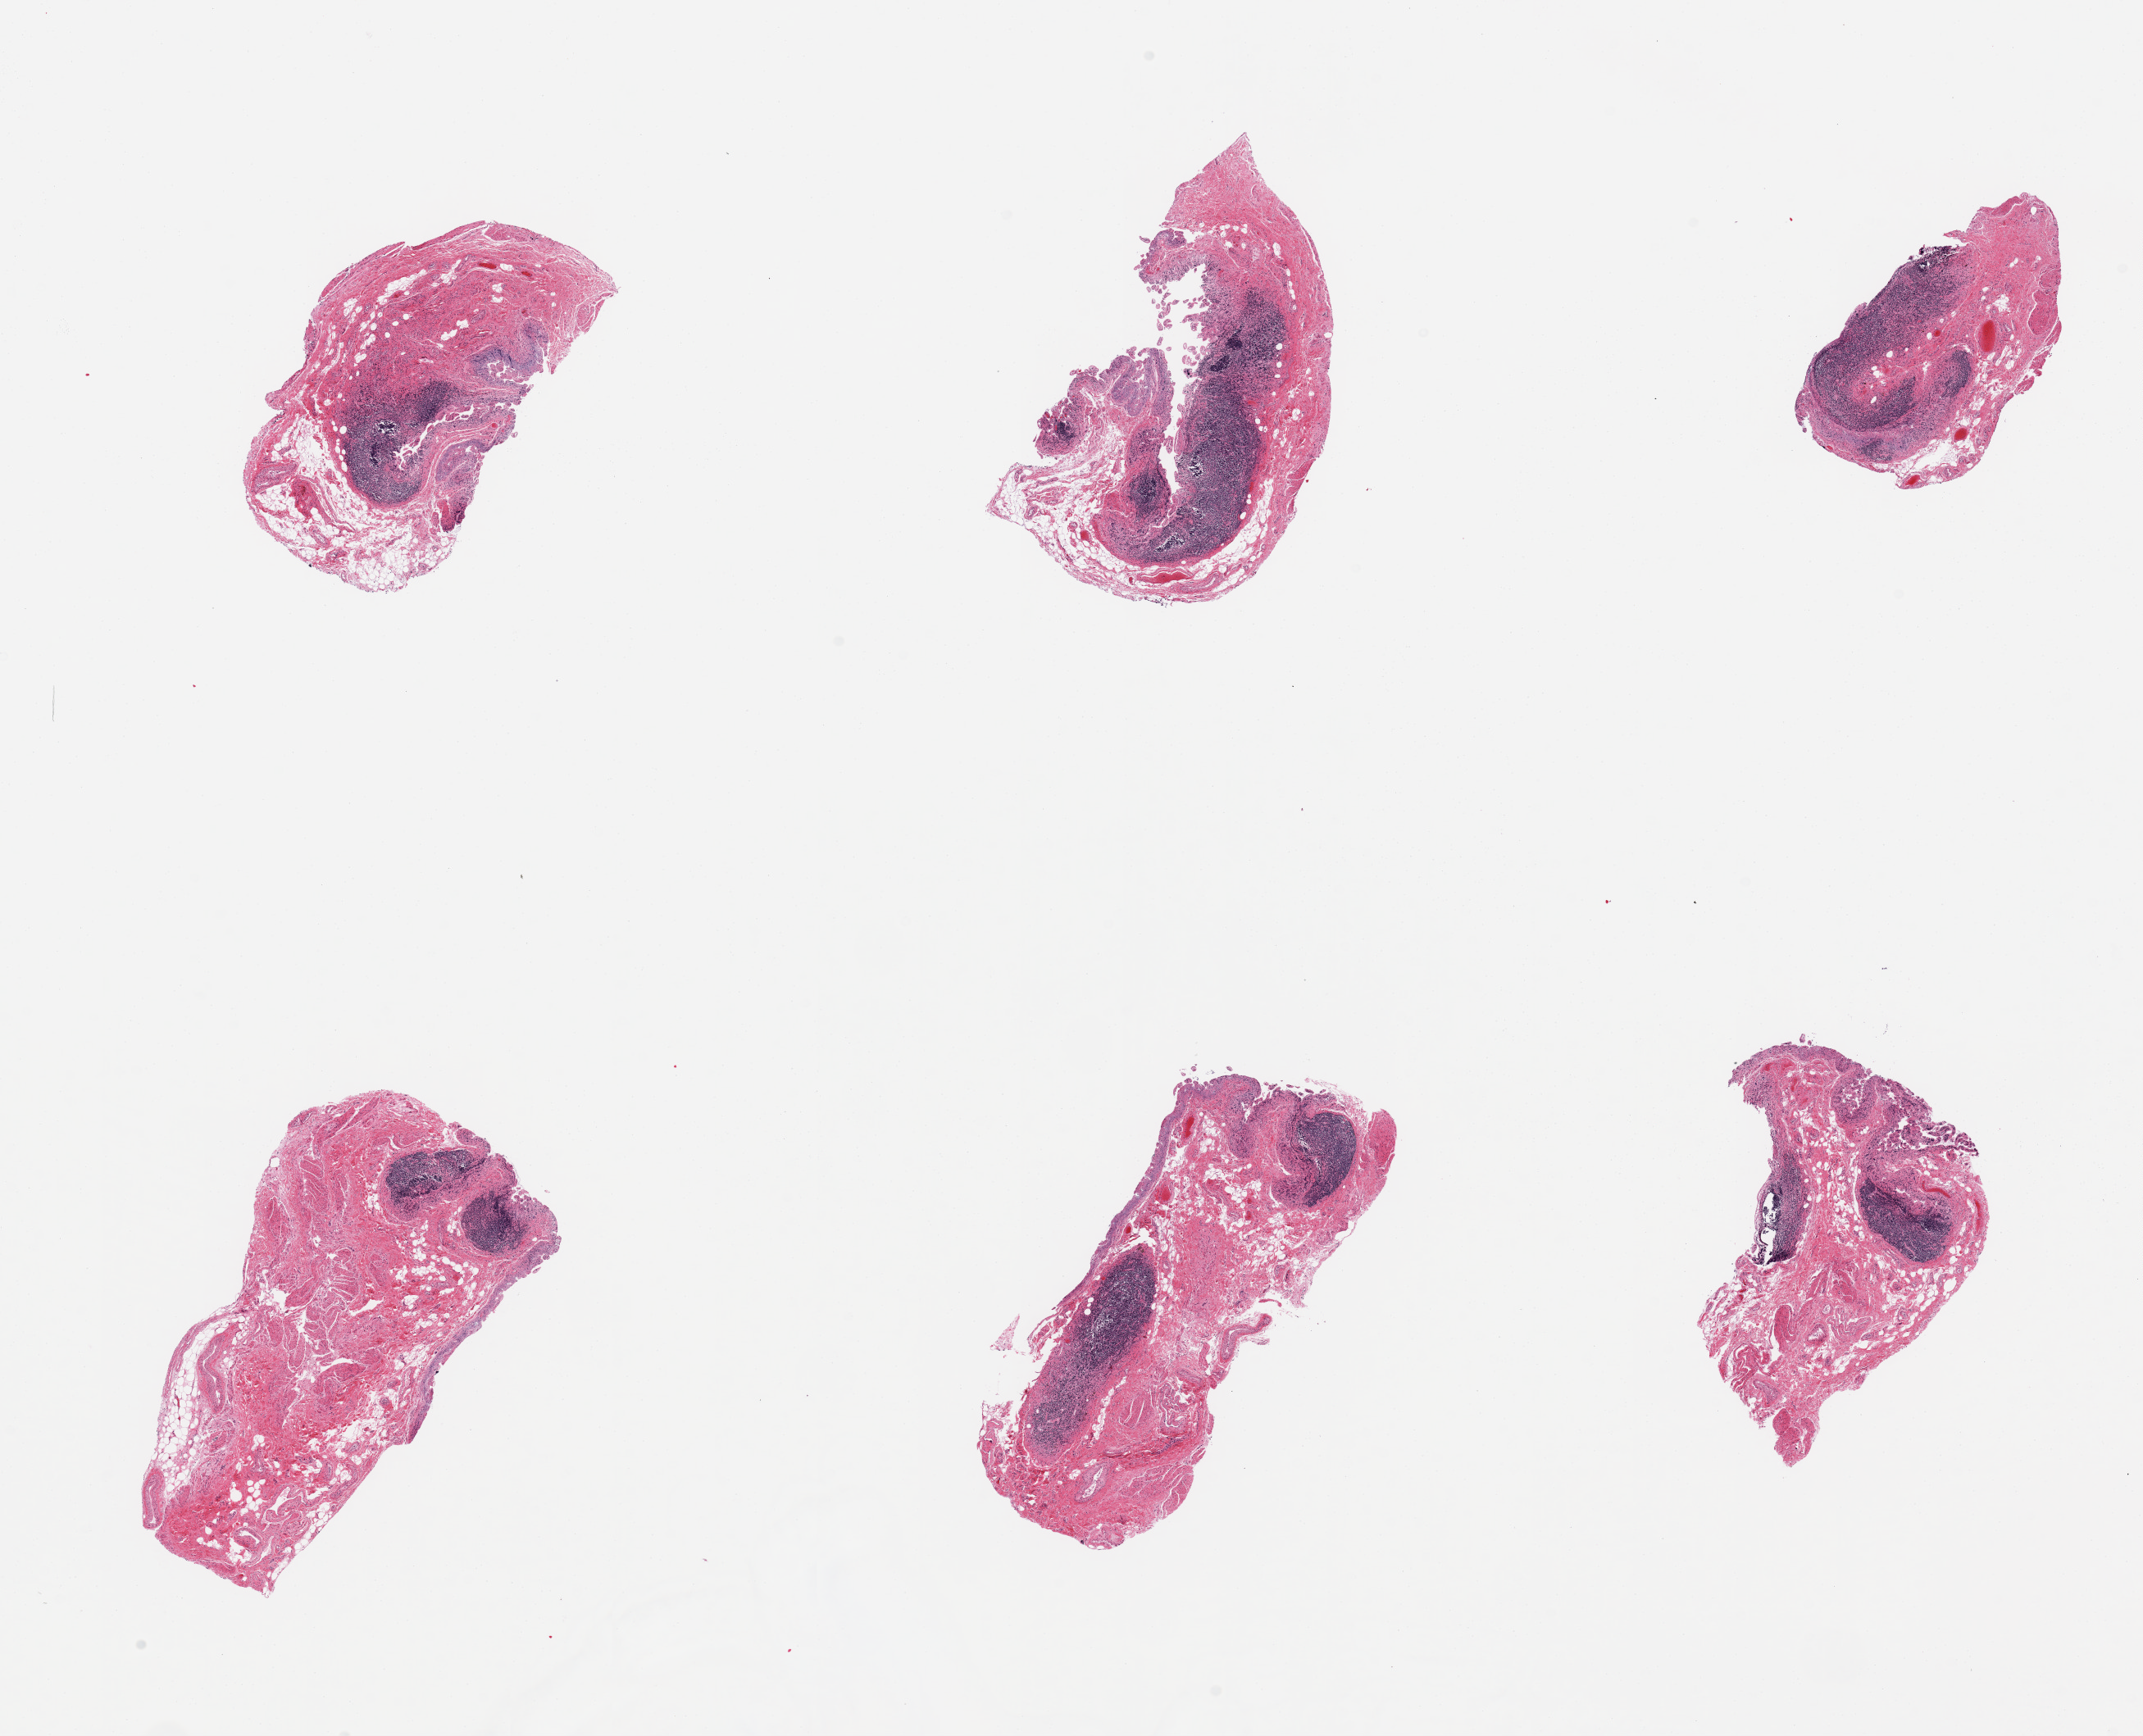
Hematoxylin and eosin (H&E) whole-slide image, low-resolution overview of the scanned area, about 20.7 x 16.8 mm; PAXgene-fixed, paraffin-embedded tissue; sampled site (target tissue): ileum; donor tissue sample.
Pathologist's review note for this sample: 6 pieces; preserved lymphoid nodules in each piece, but comprise <50%.